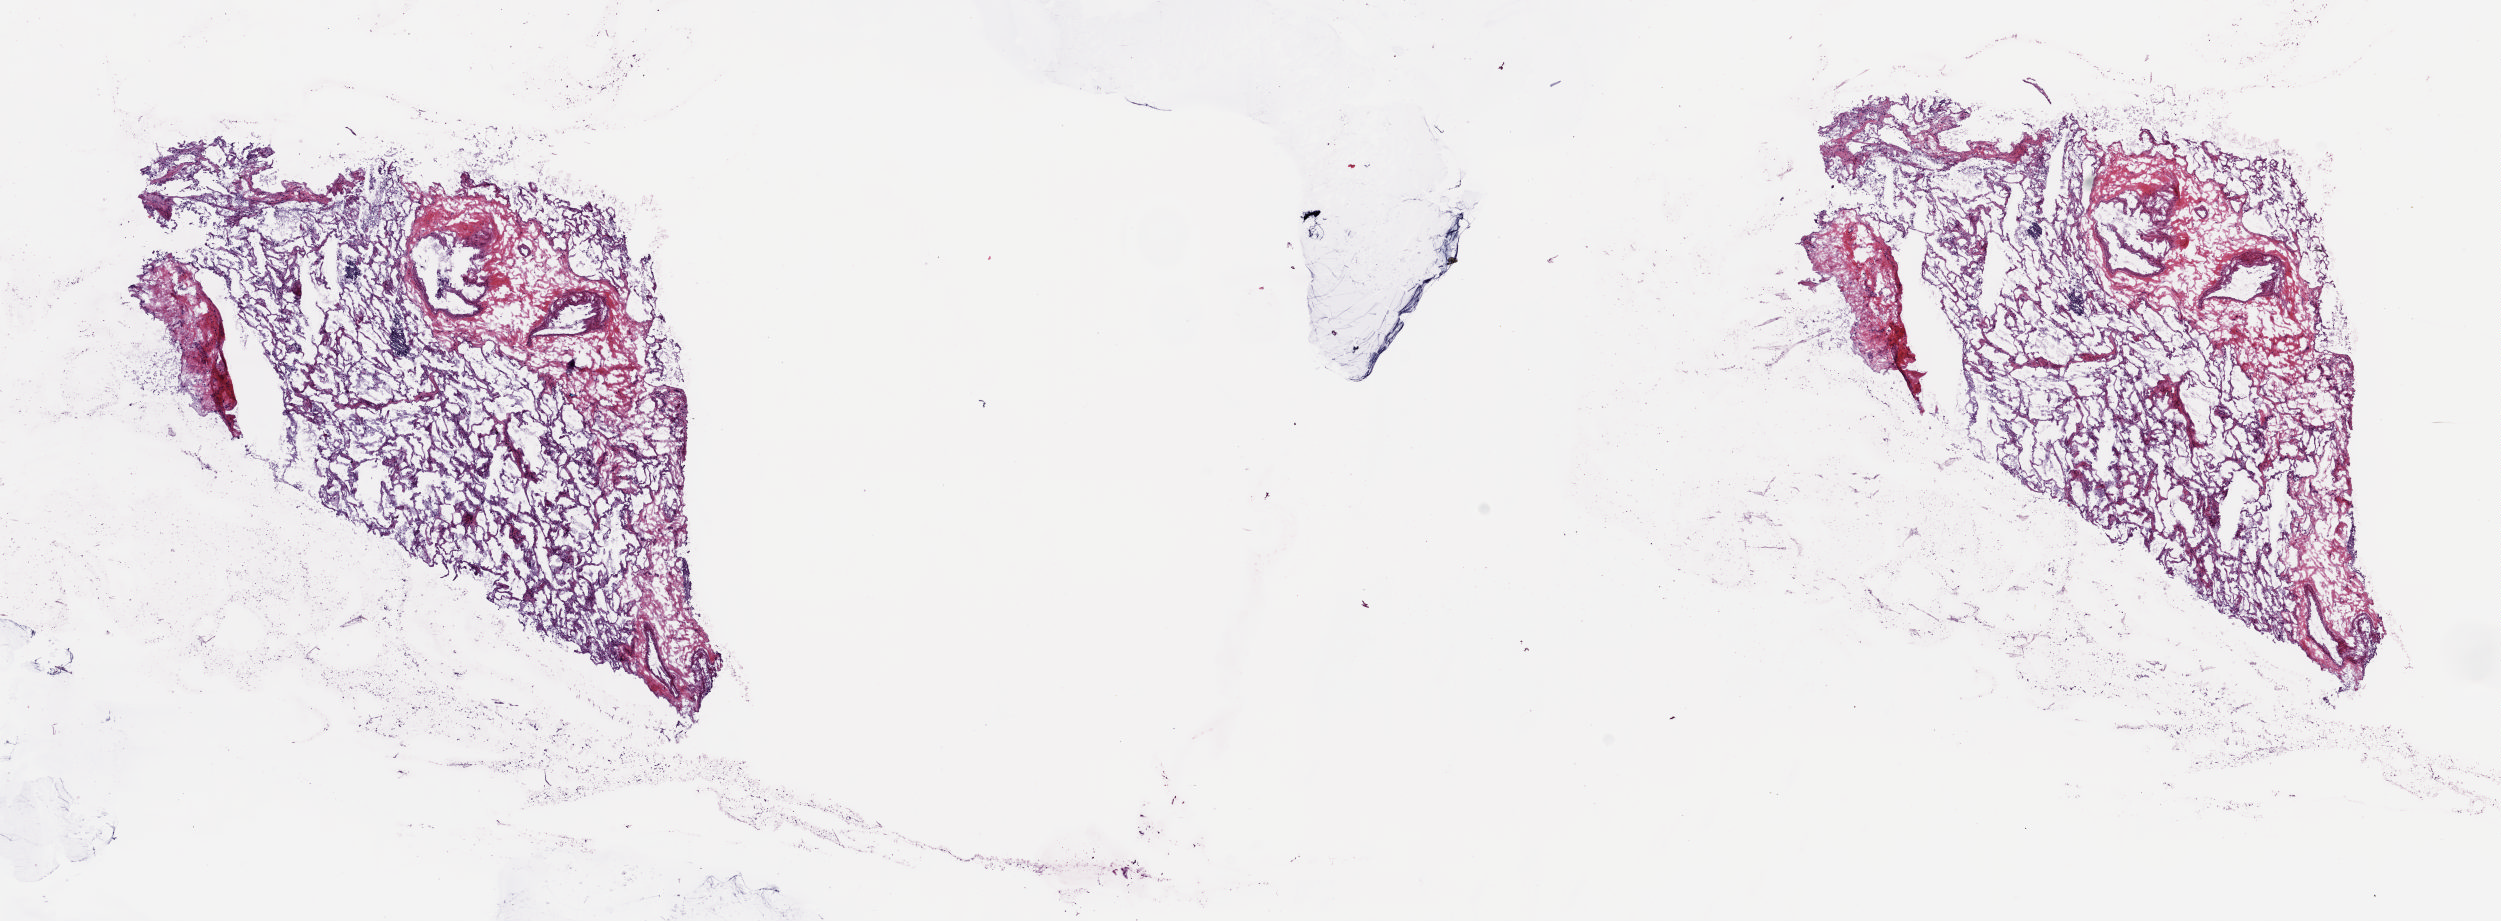
Whole-slide histology image, H&E-stained, a low-resolution overview of the entire scanned area, about 19.8 x 7.3 mm (slide scanned at 20x); frozen section from the top of the tissue portion; thymus, solid tissue normal (non-tumour tissue) sample. Male, age 64 years at initial diagnosis. Pathologist review of this section (percent, as recorded): tumour cells 0%, tumour nuclei 0%, normal cells 0%, stromal cells 100%, necrosis 0%. Infiltration values recorded for this section: lymphocyte infiltration 8%, monocyte infiltration 1%, neutrophil infiltration 2%.
* this section: solid tissue normal sample (biorepository sample class)
* patient diagnosis: Thymoma, type B3, malignant